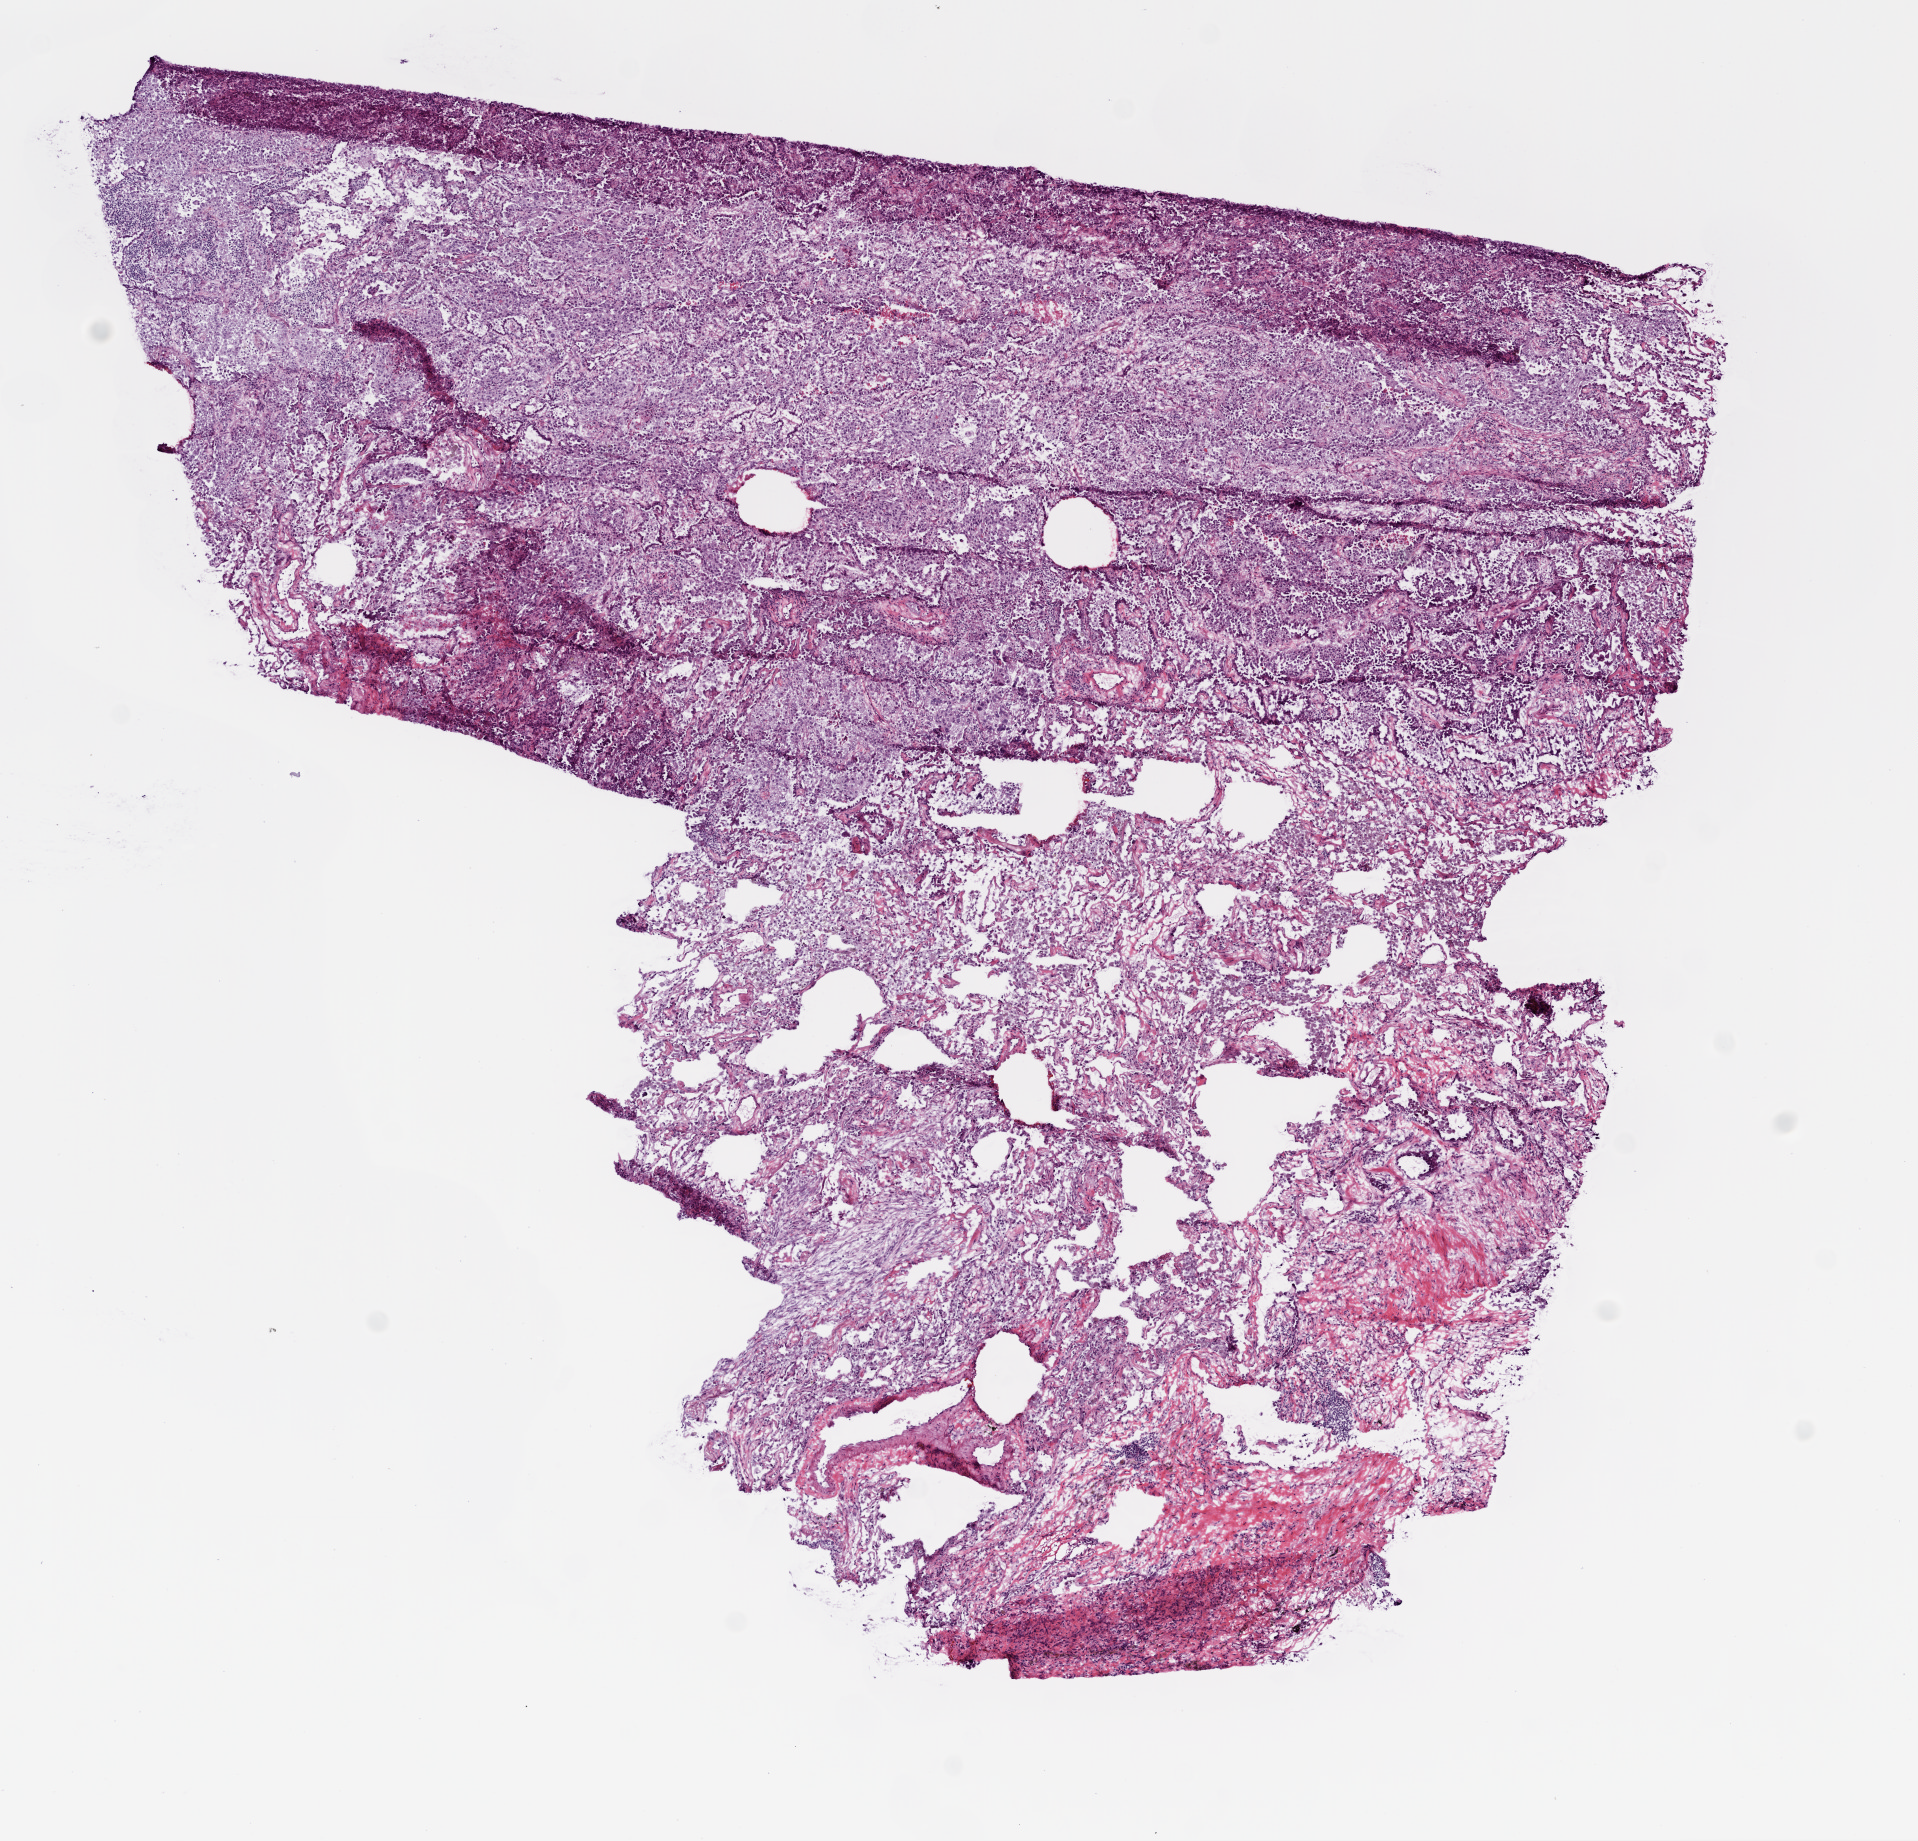
Whole-slide histology image, Hematoxylin and eosin (H&E) stained — low-resolution overview of the scanned area, about 7.7 x 7.4 mm (from a 20x scan), frozen section from the top of the tissue portion, lung, primary tumour sample. Male, age 70 years at initial diagnosis.
Pathologic diagnosis: Adenocarcinoma, NOS (upper lobe, lung).